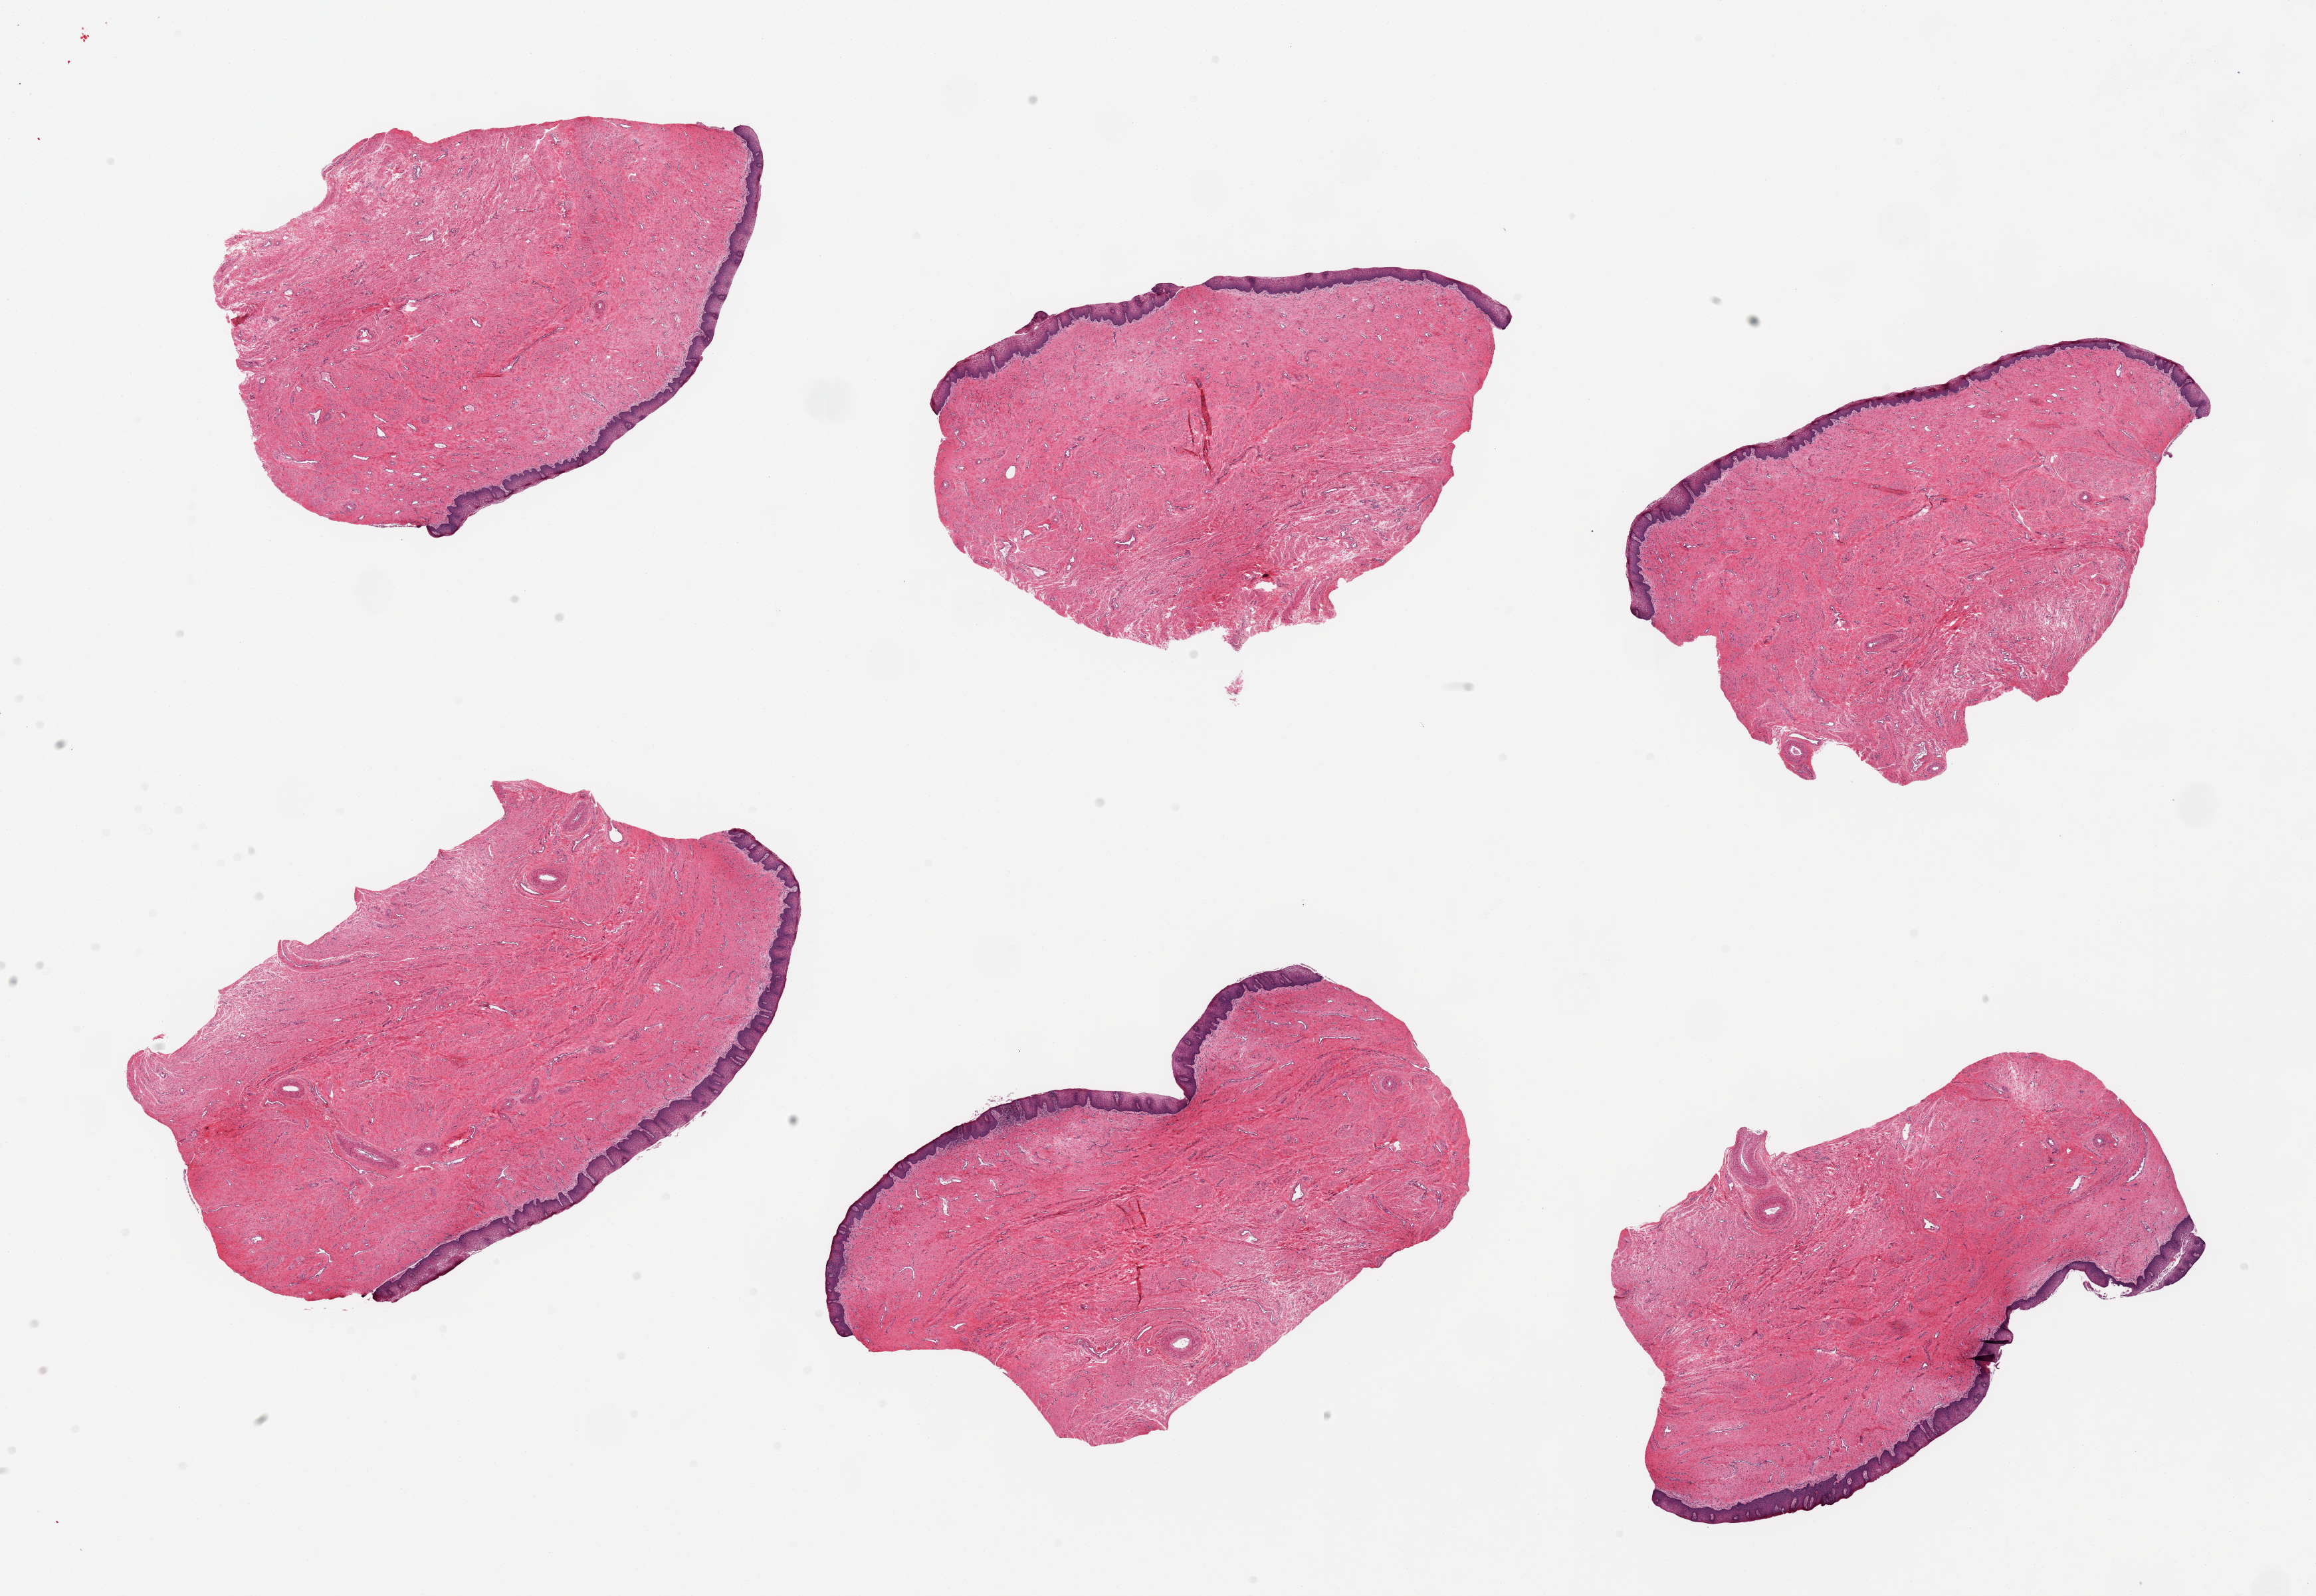
H&E whole-slide image, low-resolution overview of the scanned area, about 27.6 x 19.0 mm. PAXgene-fixed, paraffin-embedded tissue. Section of vagina (target tissue). Tissue donor sample. Donor sex: female.
• pathologist's review note for this sample: 2 pieces; focal chronic inflammation